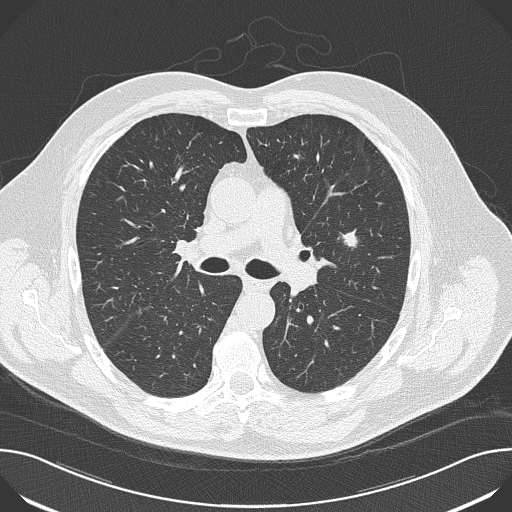
Axial slice from a low-dose chest CT screening exam, baseline annual screen, lung window (W 1500 / L -600 HU), 2 mm slice thickness, lung (sharp) reconstruction kernel (B50f), 120 kVp, slice 68 of 174 in the series, 512 × 512 image matrix, field of view 380 × 380 mm. Male participant, aged 65 years at enrolment. Former smoker at enrolment.
Expert reader's lesion annotation, box from (x=327, y=222) to (x=377, y=266) px. The screening reader recorded 5 non-calcified nodules or masses ≥4 mm on this exam (left upper lobe, left upper lobe, left upper lobe, right upper lobe, right middle lobe); which of them this box marks is not recorded. Official screen result: positive, change unspecified: nodule(s) >= 4 mm or enlarging nodule(s), mass(es), or other non-specific abnormalities suspicious for lung cancer. Later outcome: lung cancer diagnosed 52 days after this screen — adenocarcinoma, NOS, left upper lobe, moderately differentiated (G2), stage IA (AJCC 6th edition), 10 mm at pathology.